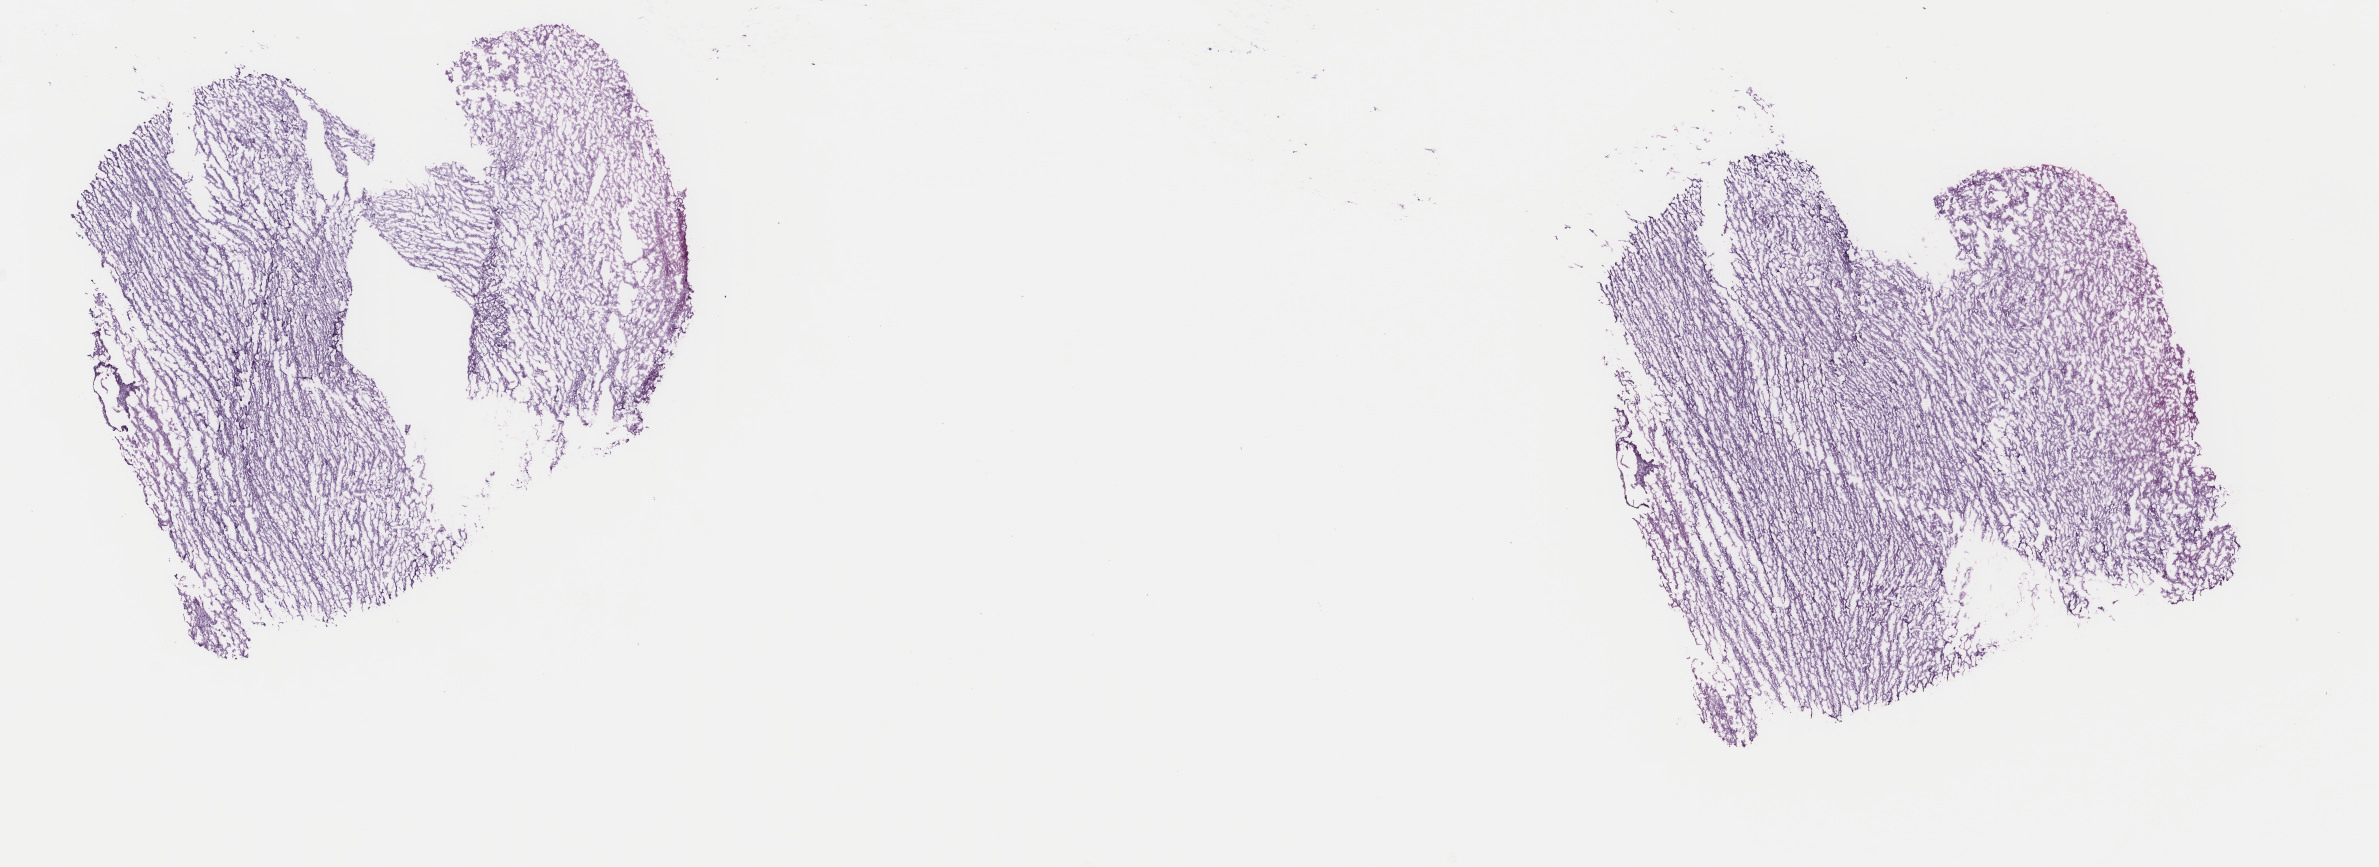
Digitized H&E tissue section (whole slide) — shown as a low-resolution overview of the whole scanned area (about 18.9 x 6.9 mm). Frozen section from the top of the tissue portion. Brain, primary tumour sample. Female, age 34 years at initial diagnosis. Histologic grade: G3 (poorly differentiated). Pathologist review of this section (percent, as recorded): tumour cells 20%, tumour nuclei 70%, normal cells 10%, stromal cells 70%, necrosis 0%. Inflammatory infiltration, as recorded: lymphocyte infiltration 0%, monocyte infiltration 0%, neutrophil infiltration 0%.
- histologic diagnosis: Astrocytoma, anaplastic (cerebrum)
- laterality: right